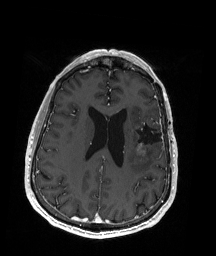
Brain MRI from a brain-tumour surgery series, one axial slice; slice 74 of 192 in the series (ordered by position); T1-weighted post-contrast; 1 mm slice thickness; 216 × 256 image matrix. Case-level facts recorded for this patient, not image findings: histopathology: Oligodendroglioma; WHO grade: 2.
Outlined on this slice (expert manual segmentation):
- previous resection cavity: bounding box [x1, y1, x2, y2] px = [132, 121, 163, 148]
- tumour: [137, 119, 154, 156]